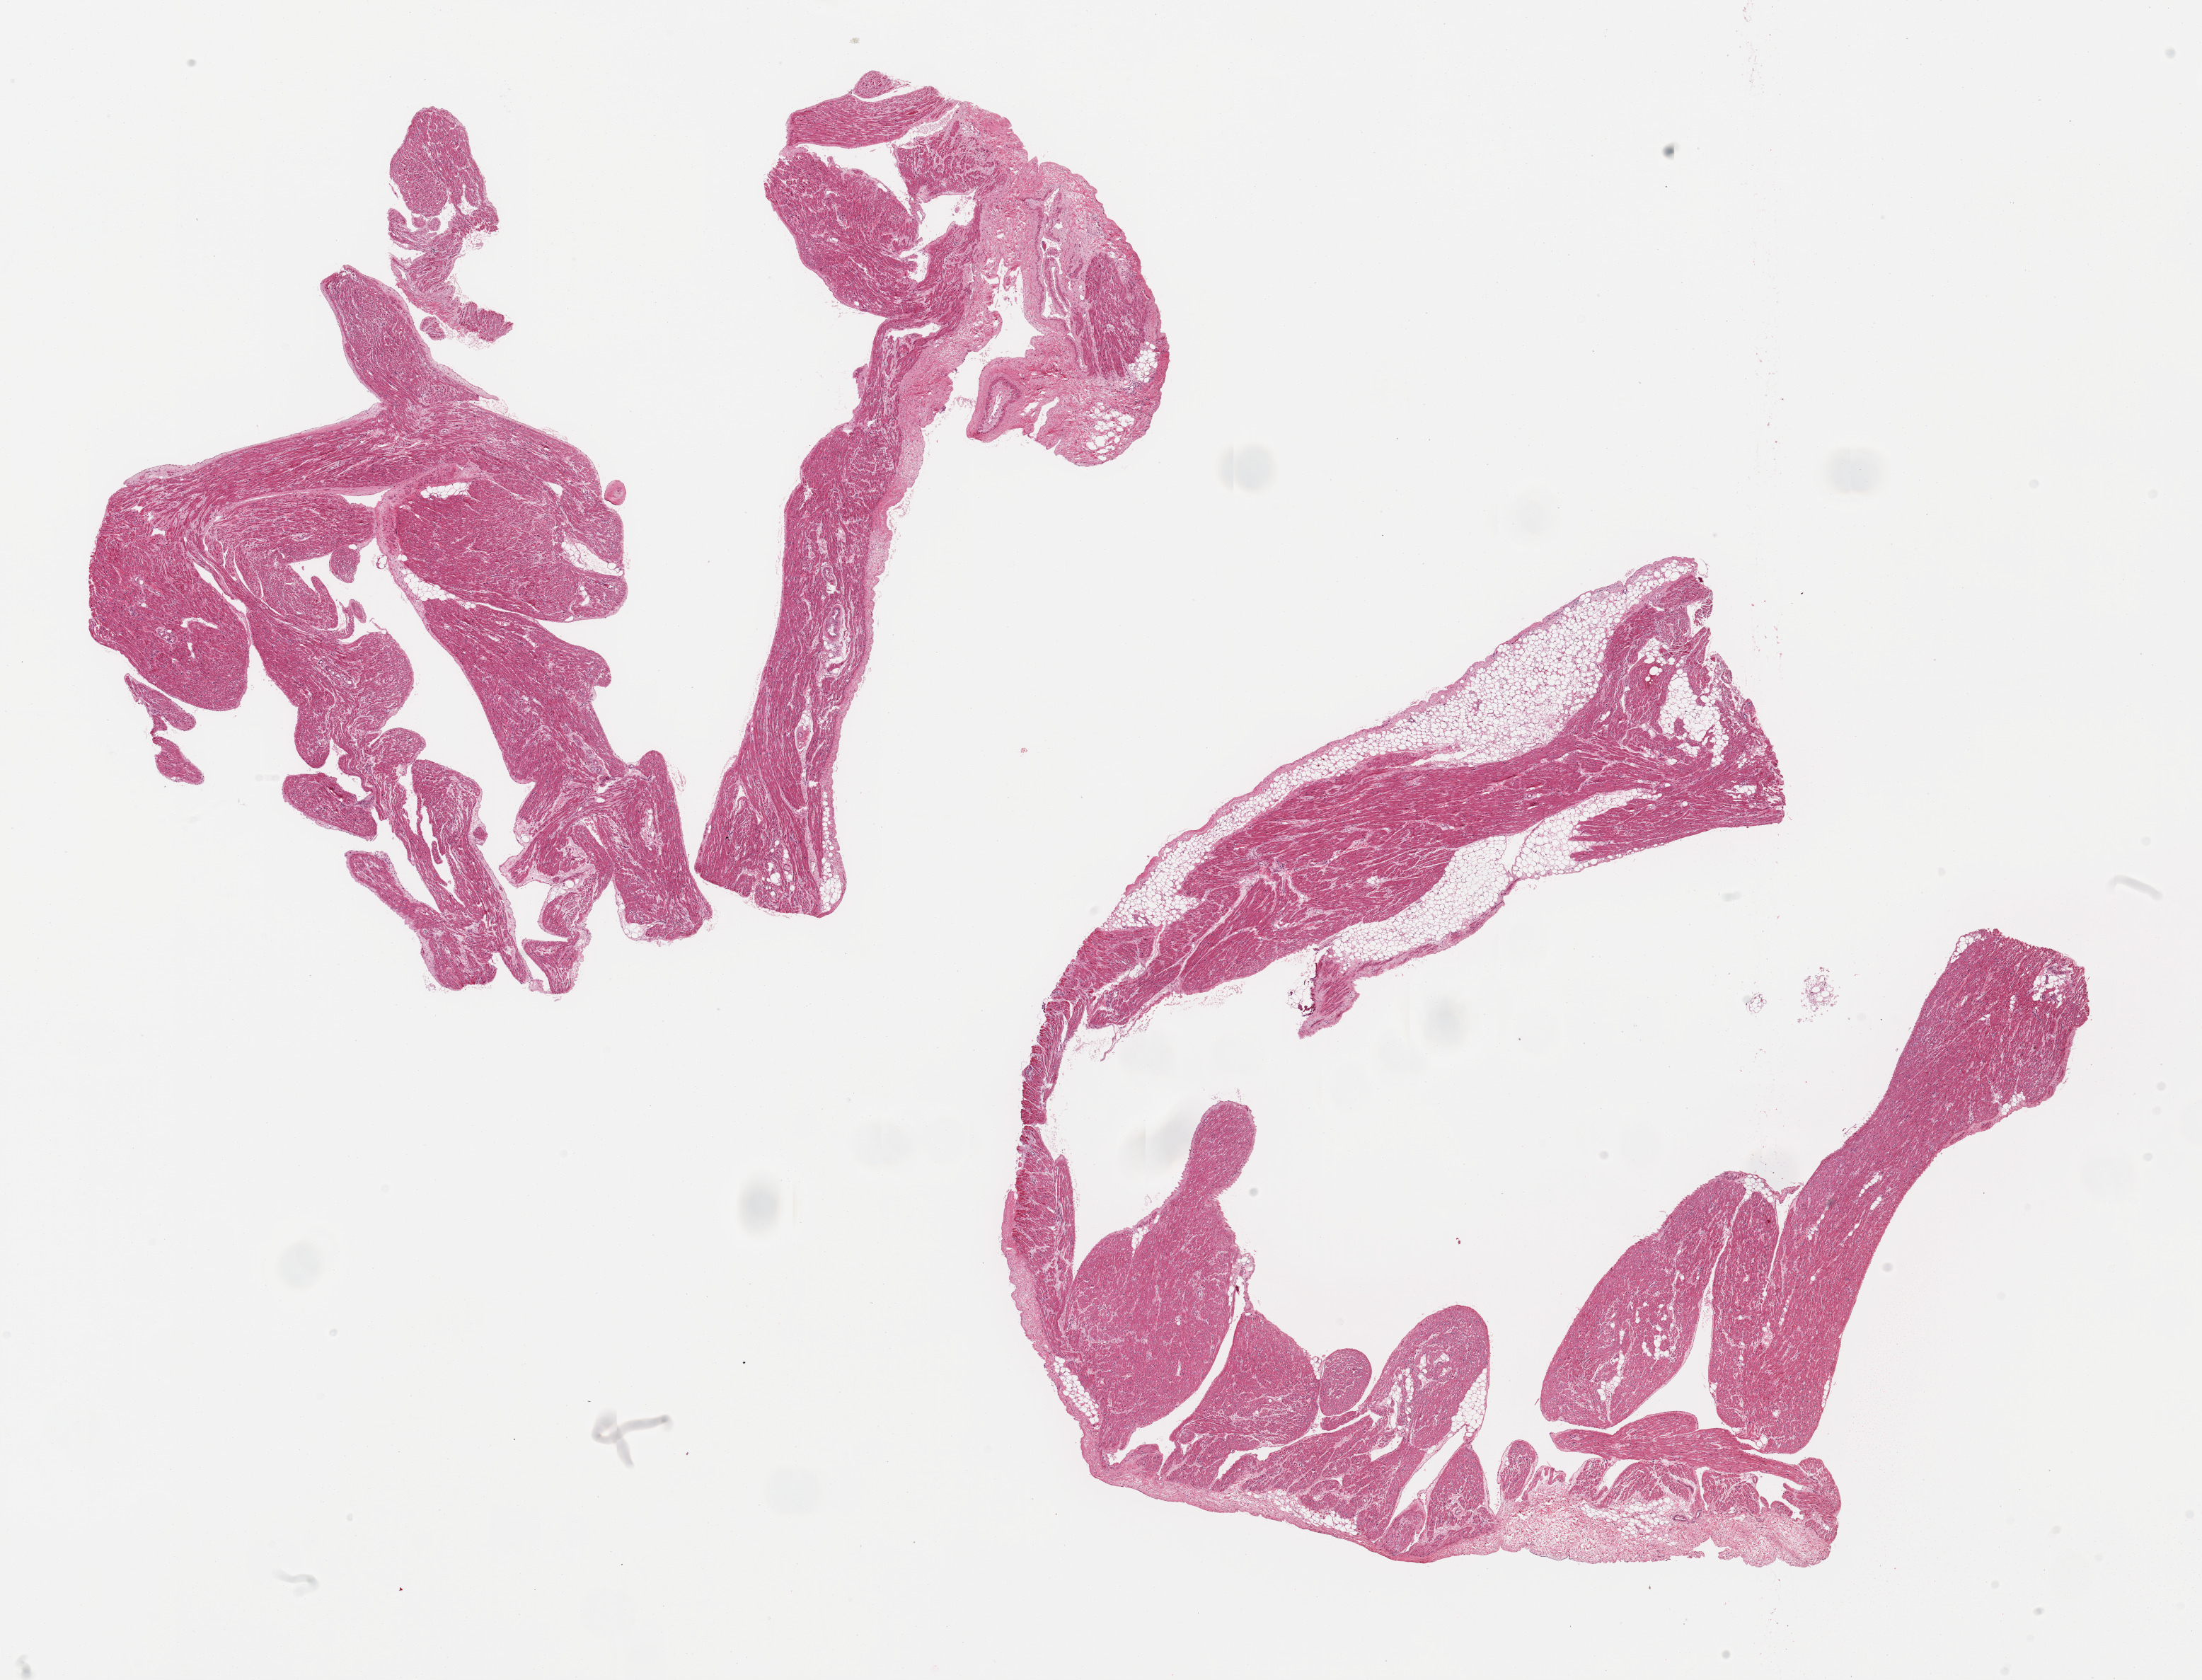
Digitized haematoxylin and eosin-stained section, whole scanned area (about 24.6 x 18.8 mm) shown as a low-resolution overview, PAXgene-fixed, paraffin-embedded tissue, target tissue: auricular appendage, donor tissue sample. Donor: female.
Reviewer comment on this tissue sample: 2 pieces, no abnormalities.